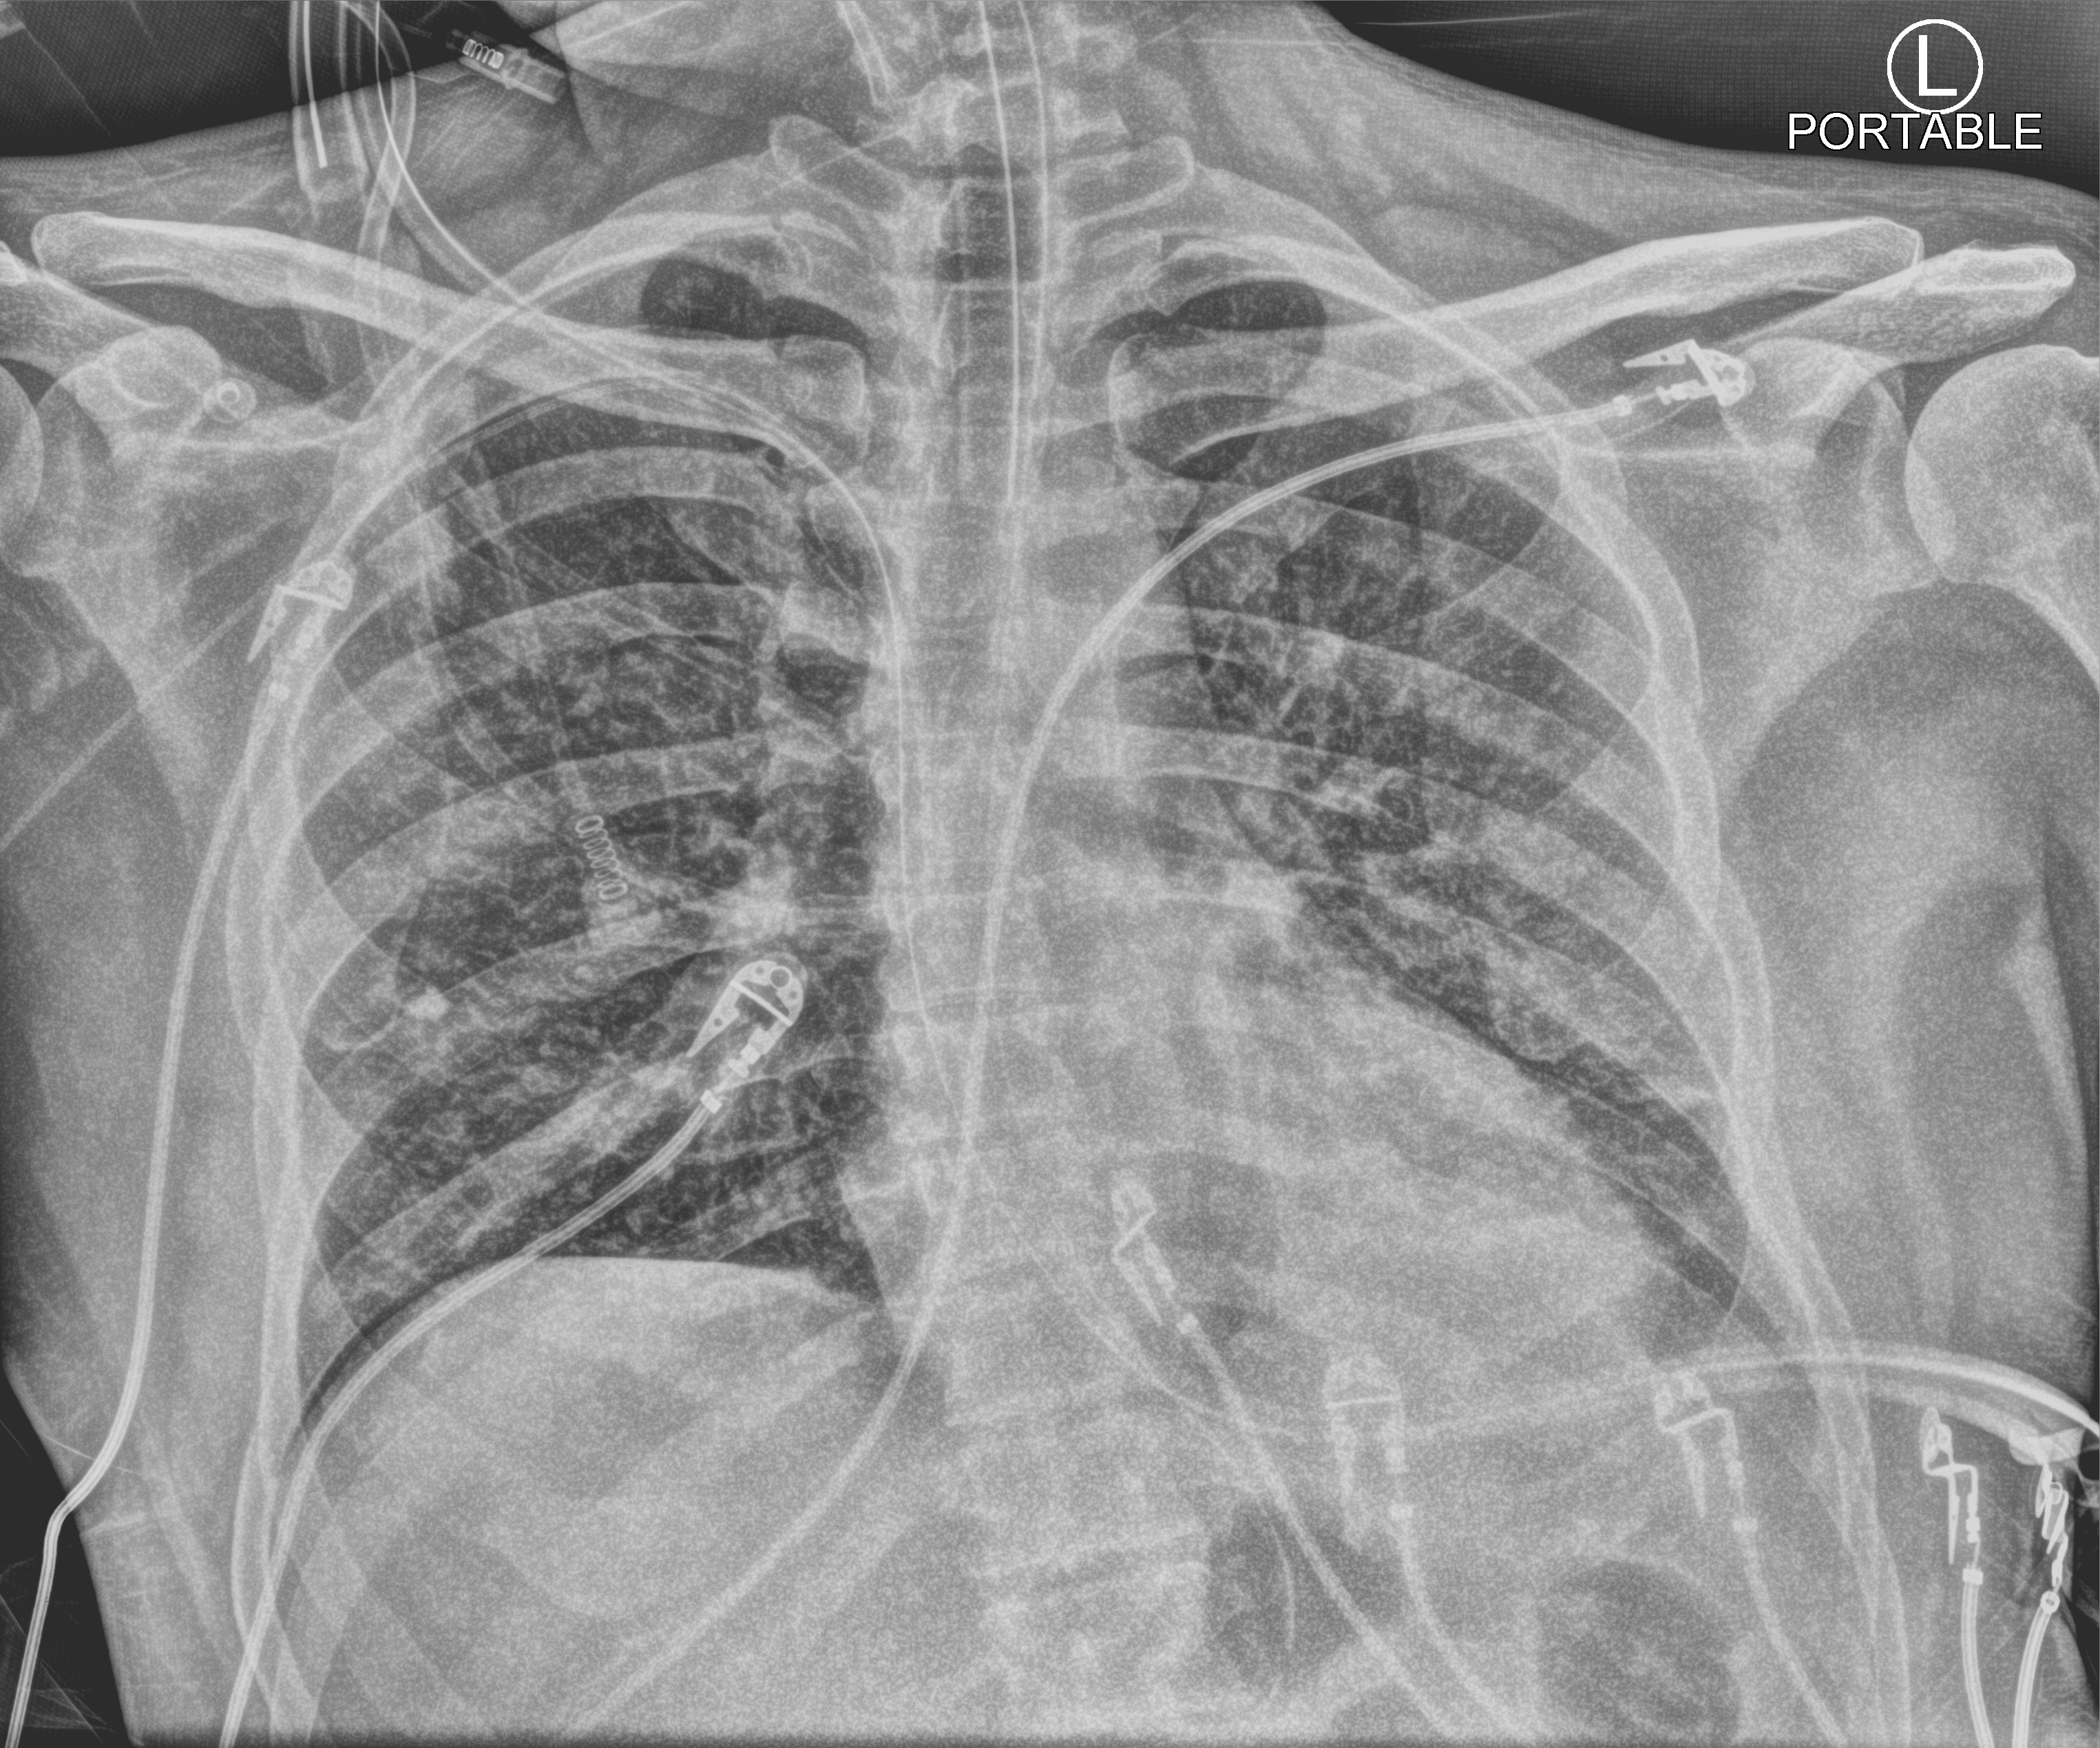
Portable chest radiograph, anteroposterior (AP) projection. Male patient hospitalised with COVID-19, age 18–59 years.
From the hospital-stay record, not from the radiograph (when in the stay this image was taken is not recorded): admitted to intensive care during this hospital stay: no.